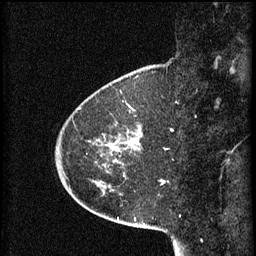
Breast MRI (dynamic contrast-enhanced), one sagittal slice; position 16 of 60 along the scan axis; 3 images stored at this slice position (order not interpretable as contrast timing); 1.5 T; TE 4.2 ms, TR 8.2 ms; 256 × 256 image matrix. Patient: female, 45 years.
Outlined on this slice (semi-automatic segmentation, software-assisted and operator-edited):
- analysis volume of interest (the breast-tissue region the enhancement analysis was run in; not a lesion): box from (x=80, y=102) to (x=142, y=167) px
- tumour enhancement mask (voxels above the 70 % enhancement threshold inside the analysis volume of interest): (x=112, y=146)–(x=116, y=163)